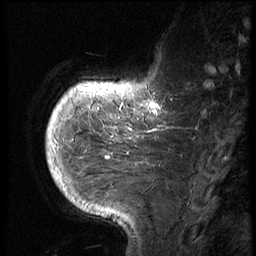
Breast MRI (dynamic contrast-enhanced), one sagittal slice; slice 16 of 72 in the series (ordered by position); 3 images stored at this slice position (order not interpretable as contrast timing); 1.5 T; TE 4.2 ms, TR 8.9 ms; 2.5 mm slice thickness; 256 × 256 image matrix, field of view 200 × 200 mm. Patient: female, 56 years. From the clinical record (not read from this slice): setting: breast cancer imaged before/during neoadjuvant chemotherapy.
Annotated regions visible in this slice (semi-automatic segmentation, software-assisted and operator-edited):
- analysis volume of interest (the breast-tissue region the enhancement analysis was run in; not a lesion): bounding box (x1, y1, x2, y2) in pixels: (114, 76, 177, 138)
- tumour enhancement mask (voxels above the 140 % enhancement threshold inside the analysis volume of interest): (130, 95, 161, 133)